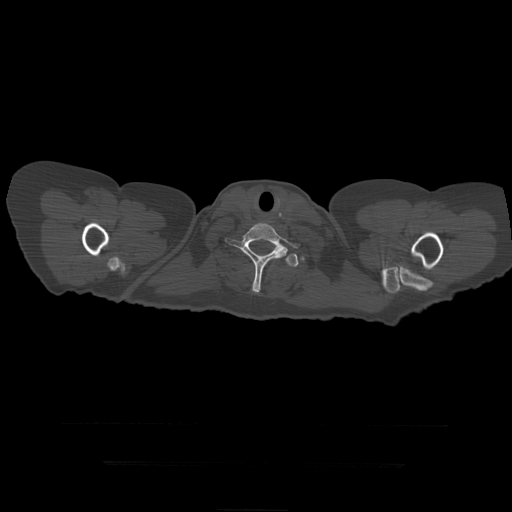
CT including the spine, one axial slice. Position 387 of 399 along the scan axis. Reconstruction kernel STANDARD. Bone window (W 1800 / L 400 HU). 512 × 512 image matrix. Patient age 41 years. From the clinical record (not read from this slice): primary cancer: breast.
Annotated regions visible in this slice (semi-automatically segmented with operator editing):
- T1 vertebra: bounding box [x1, y1, x2, y2] px = [225, 223, 298, 293]
- T2 vertebra: [286, 254, 299, 267]